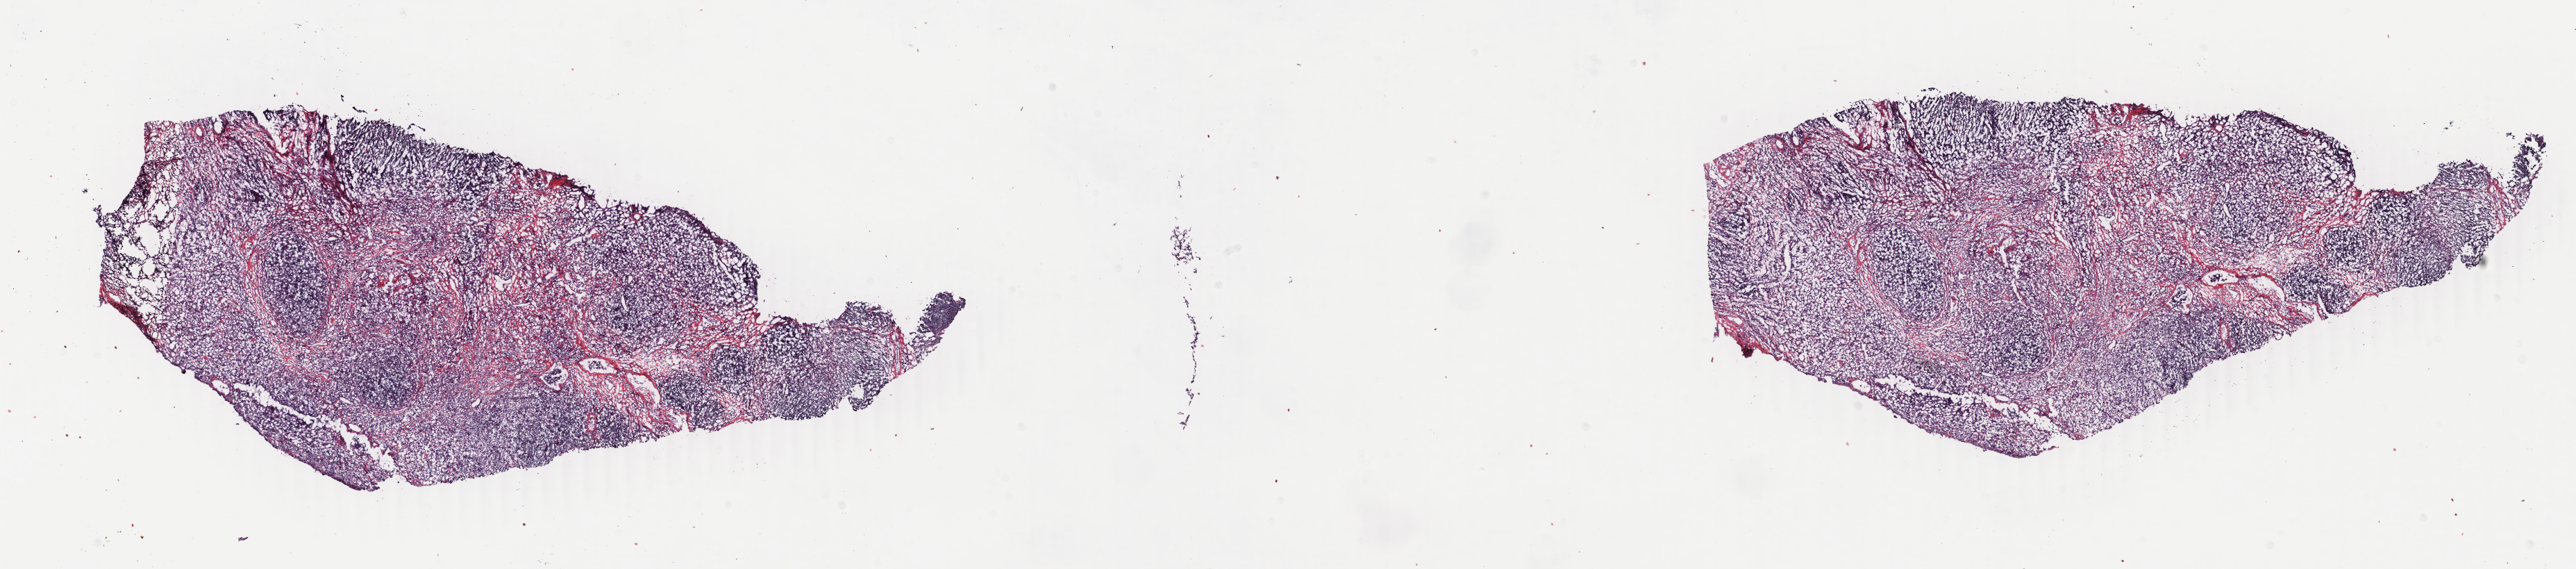
Digitized Hematoxylin and eosin (H&E) stained tissue section (whole slide) — shown as a low-resolution overview of the whole scanned area (about 29.5 x 6.5 mm); frozen section; breast, primary tumour sample. Female, age 39 years at initial diagnosis. Composition of this section per pathologist review: tumour cells 85%, tumour nuclei 85%, normal cells 0%, stromal cells 14%, necrosis 1%. Inflammatory infiltration, as recorded: lymphocyte infiltration 4%, monocyte infiltration 0%, neutrophil infiltration 0%.
TNM: T3 N1 M0. Laterality: right. AJCC pathologic stage: IIIA. Diagnosis: Infiltrating duct carcinoma, NOS.